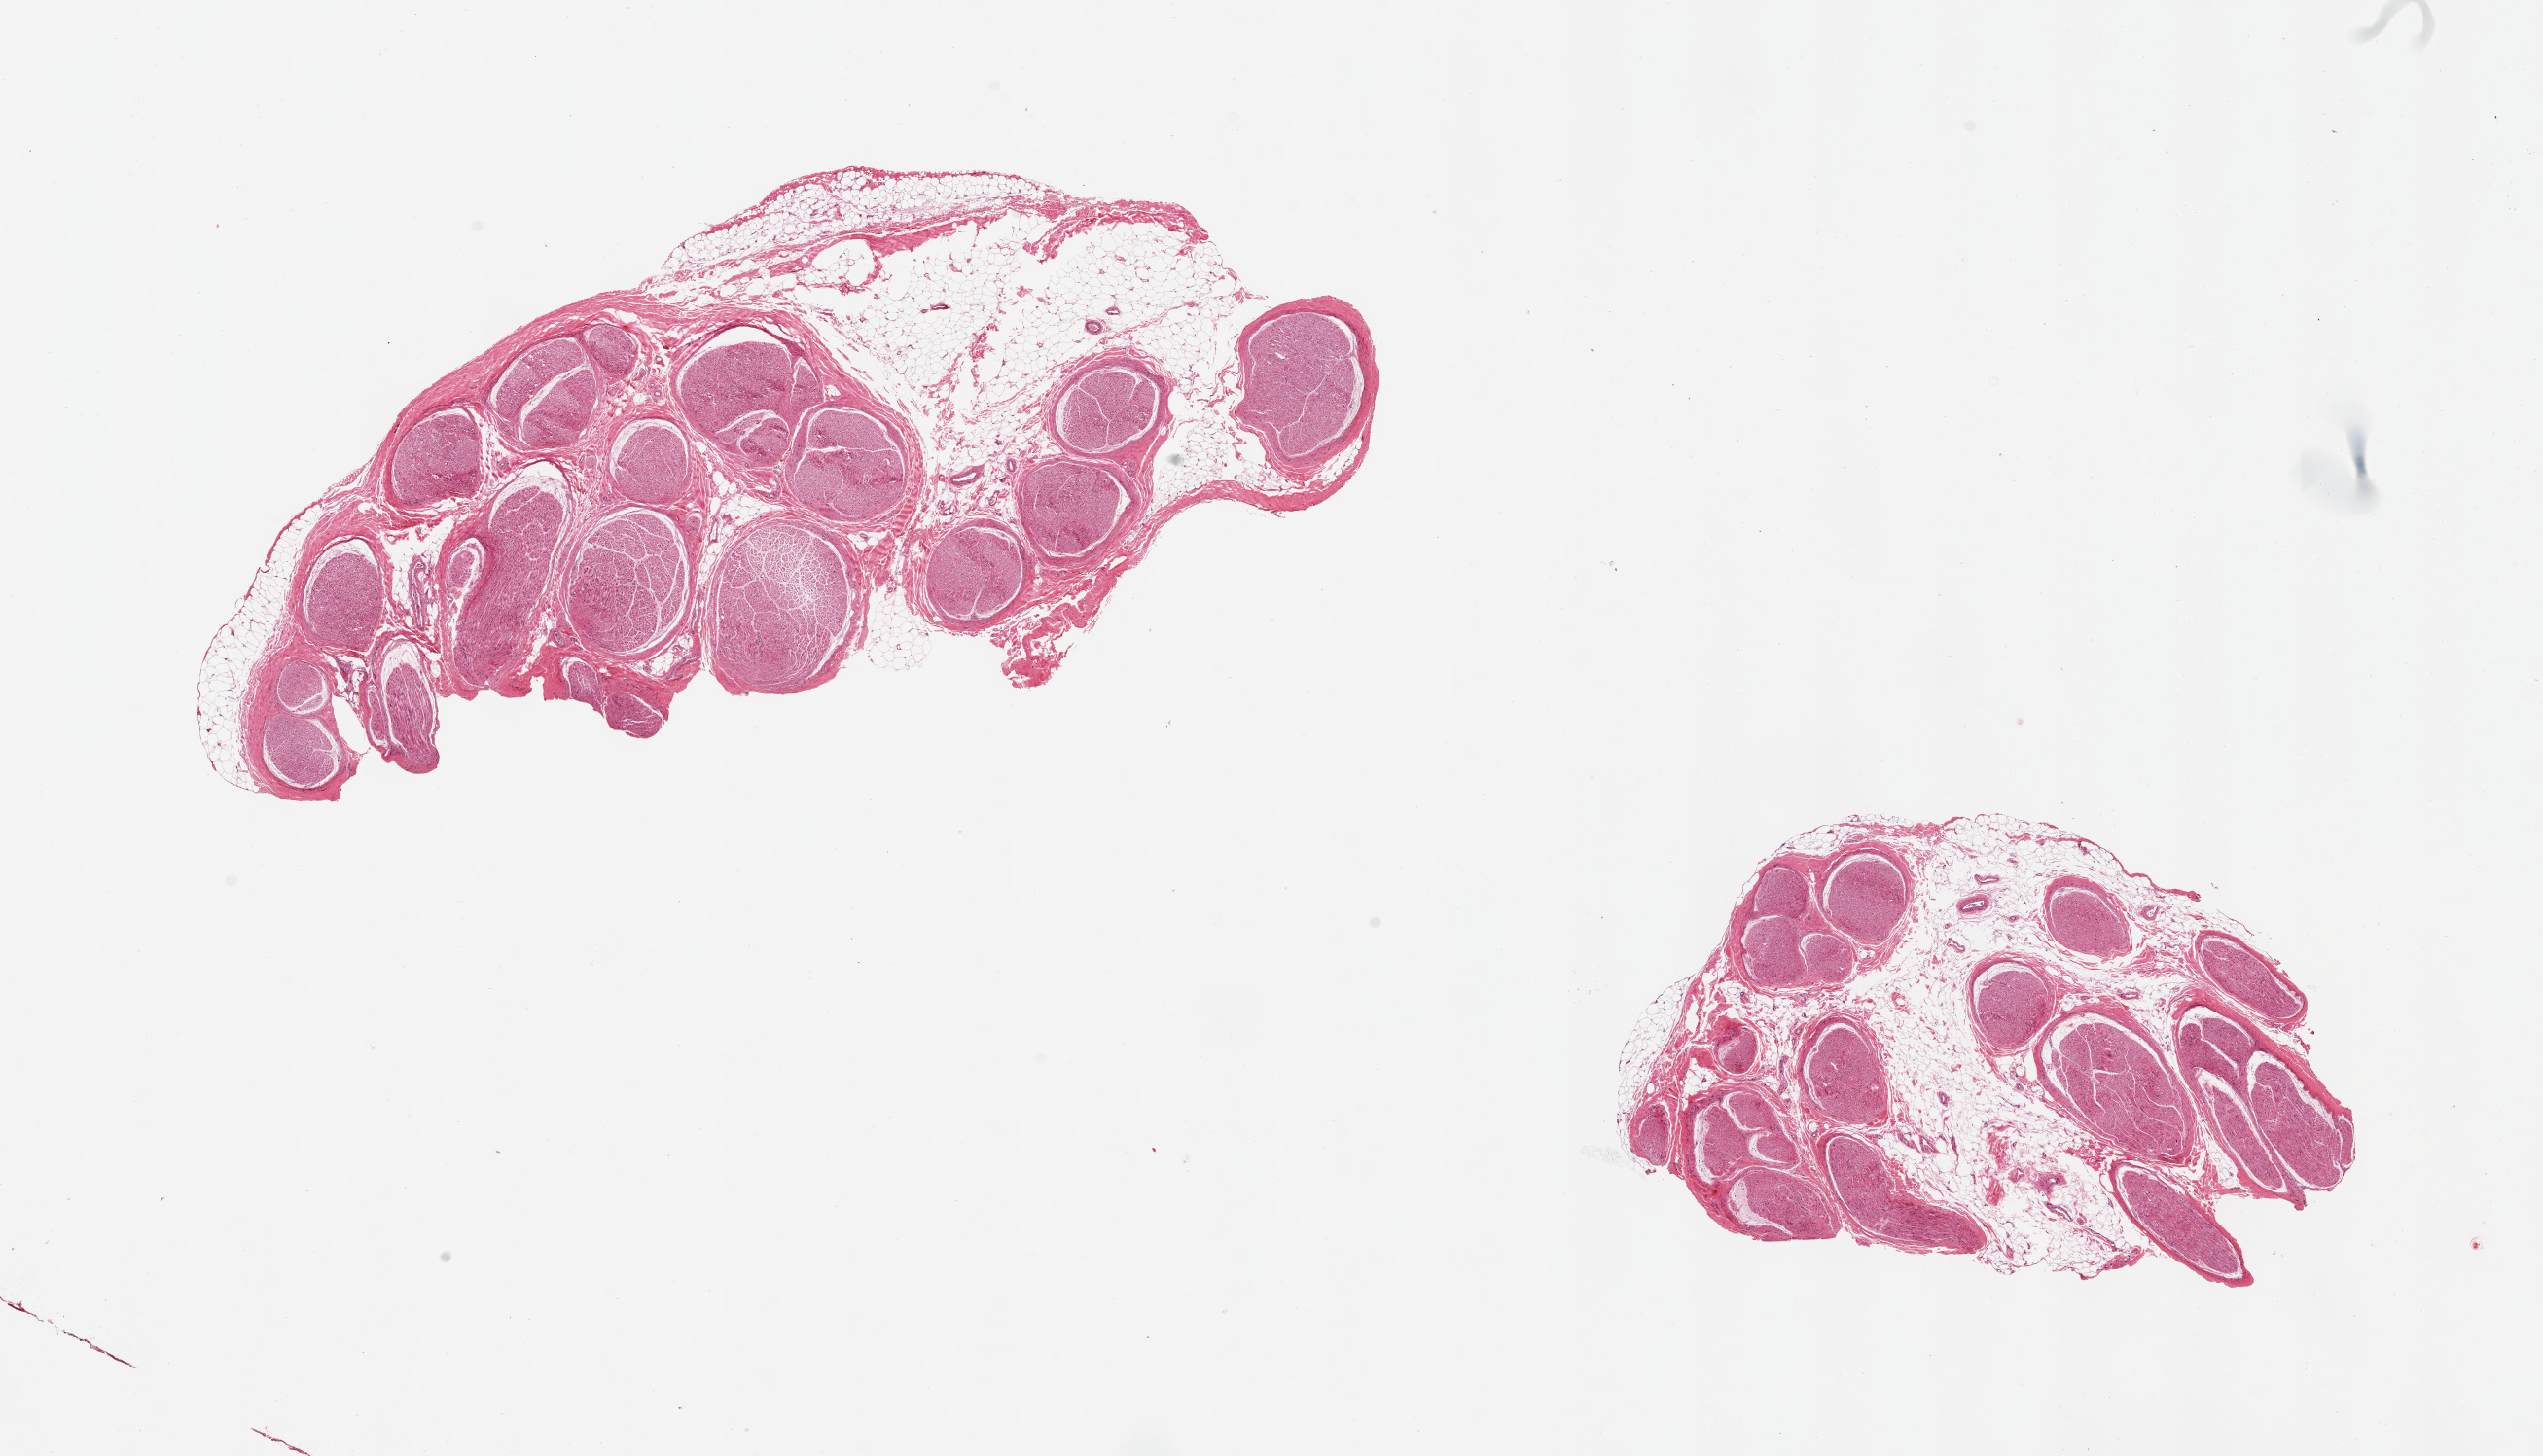
Hematoxylin and eosin (H&E) whole-slide image, shown as a low-resolution overview of the whole scanned area (about 20.7 x 11.8 mm). PAXgene-fixed paraffin-embedded (PFPE) section. Sampled site (target tissue): tibial nerve. Donor tissue sample. Male donor.
Review note (as recorded): 2 pieces; ~30% internal/external fat.